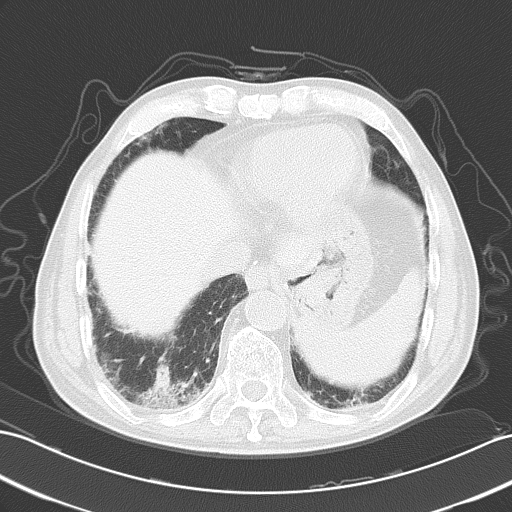
Chest CT, one axial slice; position 13 of 51 along the scan axis; reconstruction kernel B70f; 120 kVp; lung window (W 1500 / L -600 HU); 5 mm slice thickness; 512 × 512 image matrix. Male patient, age 73 years. Case-level facts recorded for this patient, not image findings: clinical TNM (as recorded): T1a N0 M0; histopathological grade: G3.
Structures marked on this image (bounding box drawn by a radiologist):
- lung tumour (recorded histology: small cell carcinoma): bounding box [x1, y1, x2, y2] px = [143, 362, 177, 399]